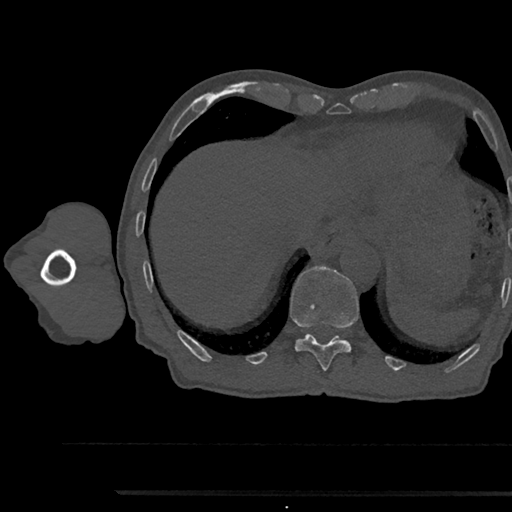
CT including the spine, one axial slice; slice 778 of 797 in the series (ordered by position); reconstruction kernel Br40s/3; 120 kVp; bone window (W 1800 / L 400 HU); 512 × 512 image matrix, field of view 367 × 367 mm. Male patient, age 79 years. From the clinical record (not read from this slice): primary cancer: prostate.
Structures marked on this image (semi-automatically segmented with operator editing):
- T11 vertebra: box from (x=290, y=266) to (x=359, y=372) px